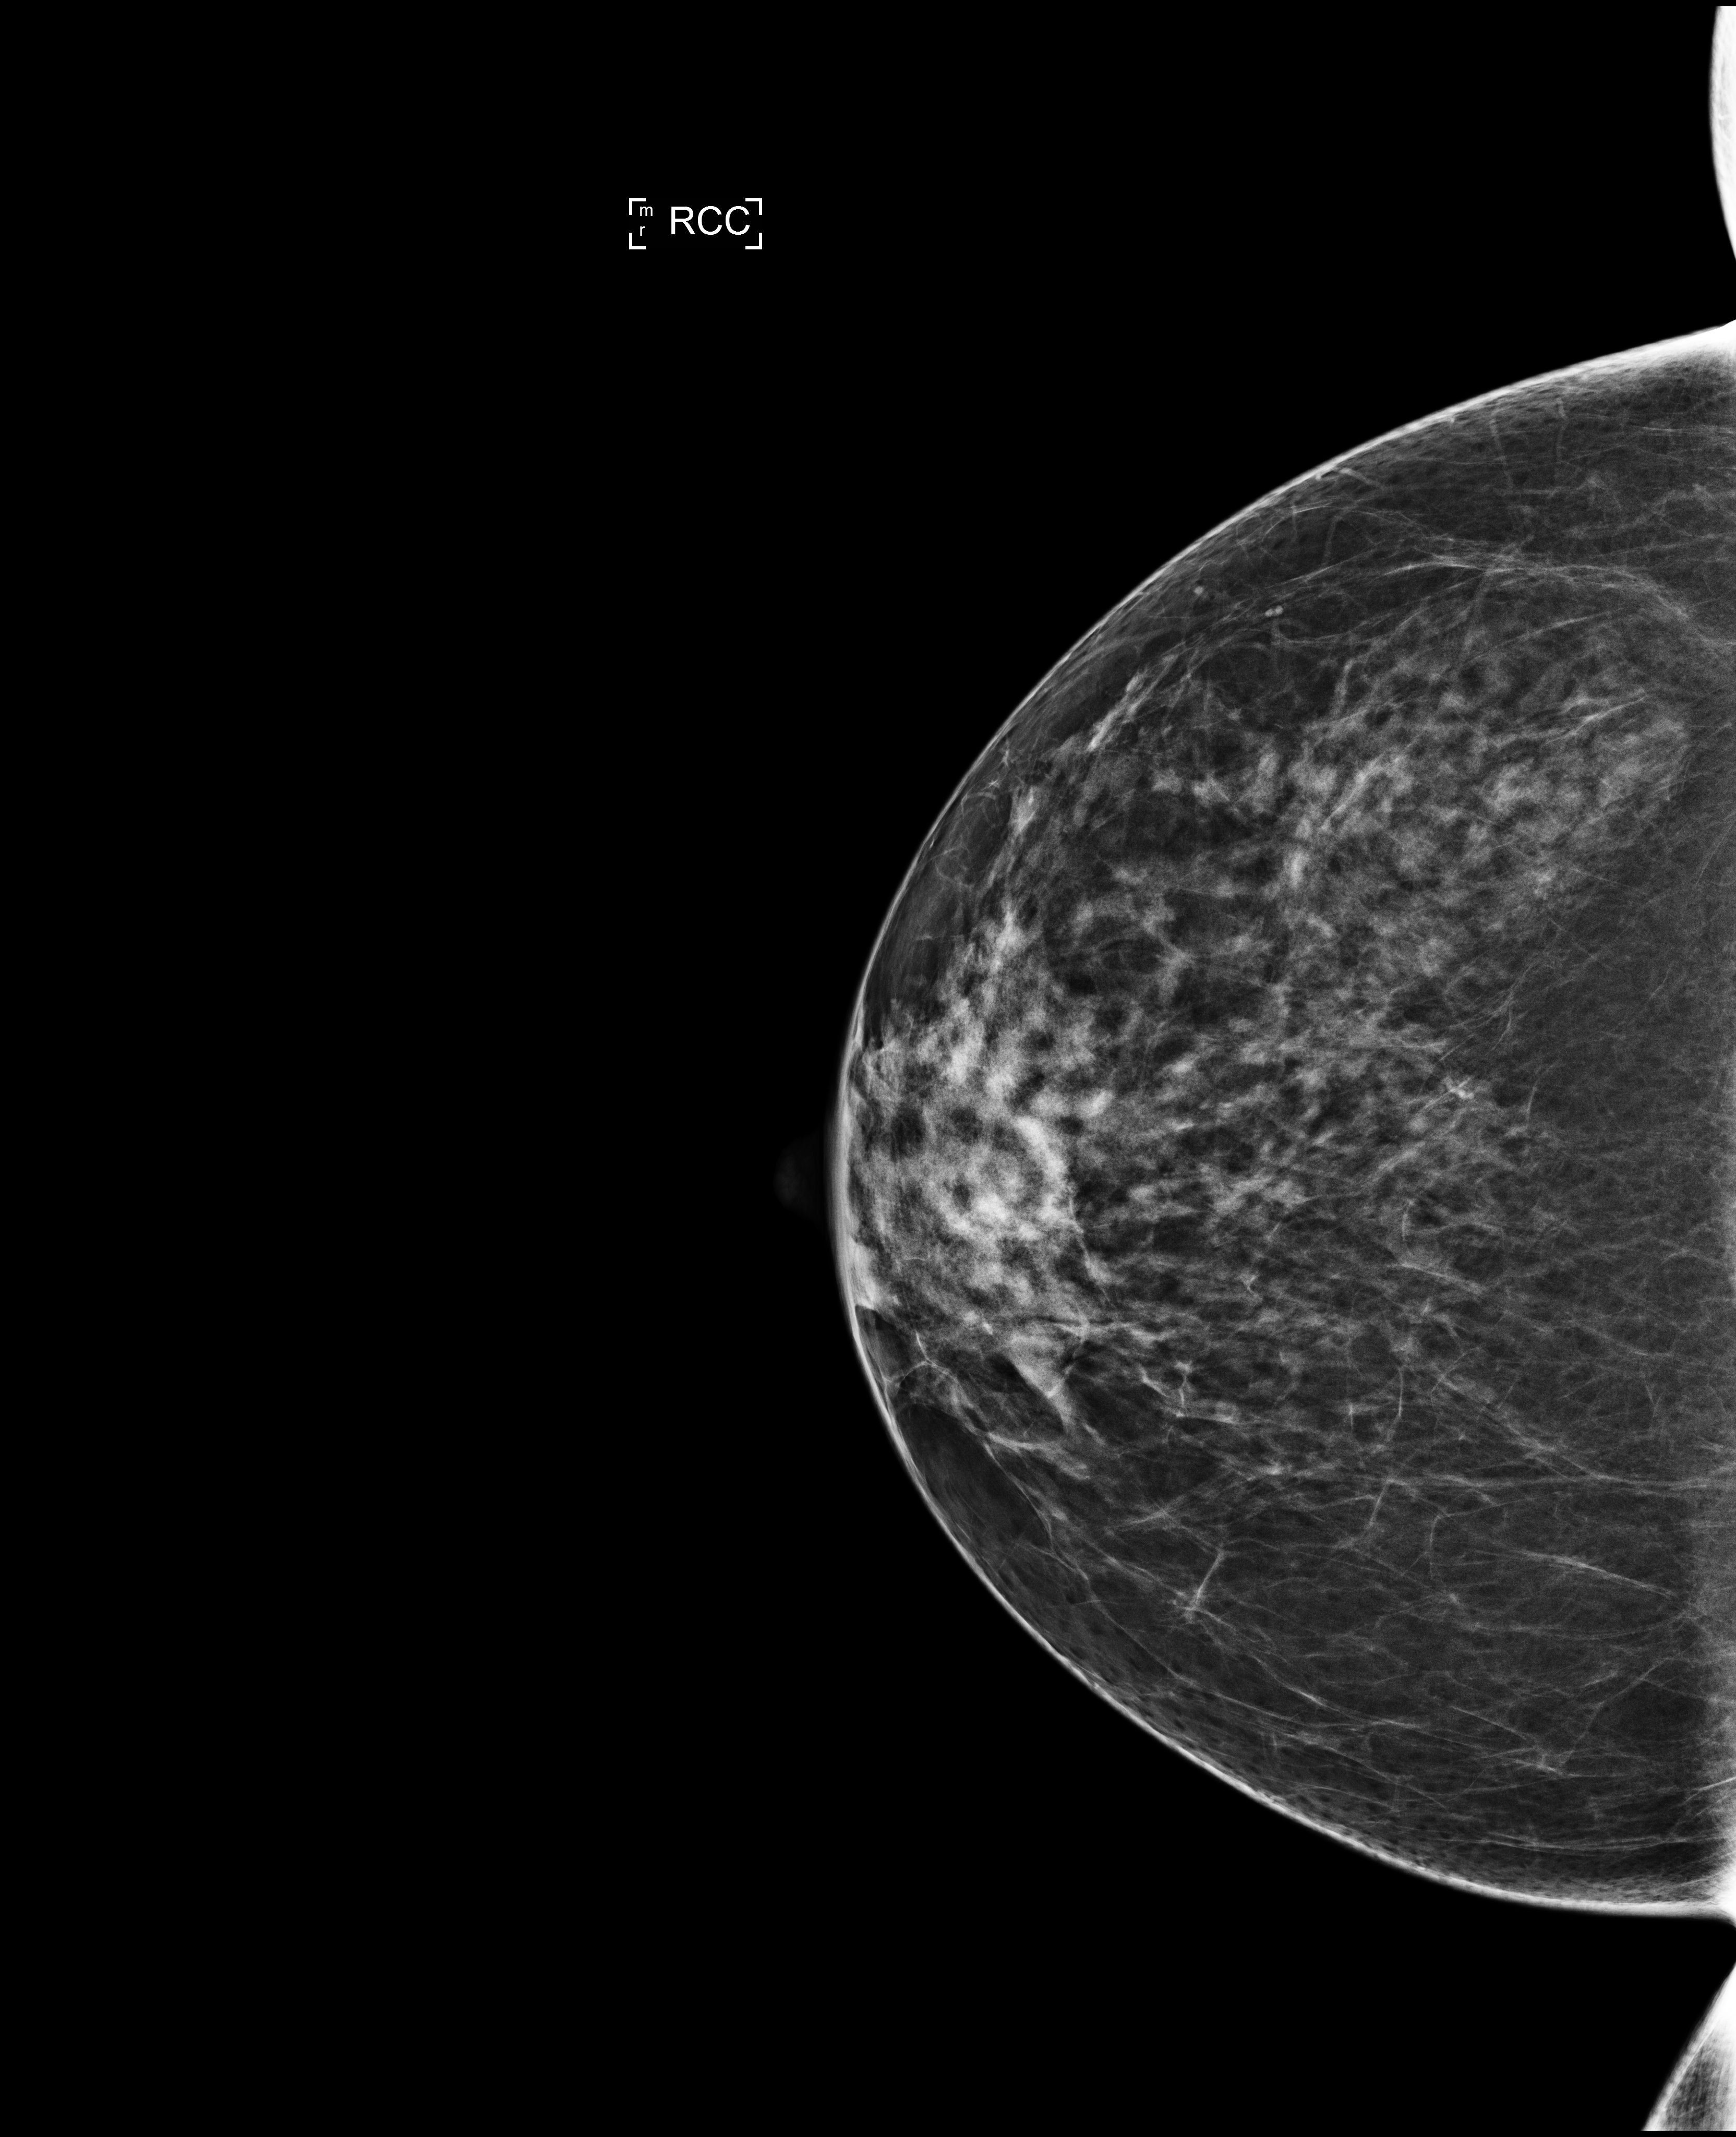
Screening examination. Female patient, age 53 years.
Image type: full-field digital mammogram. Breast: right. Projection: cranio-caudal projection.